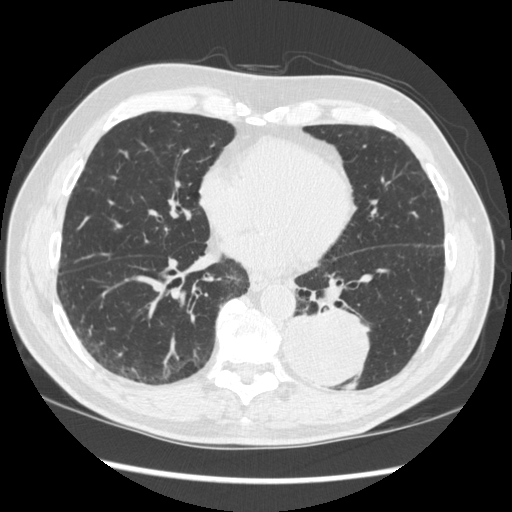
Low-dose screening chest CT, axial slice, first (baseline) screen, lung window (W 1500 / L -600 HU), slice 132 of 348 in the series. Male participant, aged 72 years at enrolment. Current smoker at enrolment.
Expert-annotated lung lesion, bounding box (x1, y1, x2, y2) in pixels: (271, 299, 375, 389). The screening reader recorded 2 non-calcified nodules or masses ≥4 mm on this exam (left lower lobe, right middle lobe); which of them this box marks is not recorded. Lung cancer was diagnosed 37 days after this screen: squamous cell carcinoma, NOS, left lower lobe, stage IIIA (AJCC 6th edition), 60 mm at pathology.